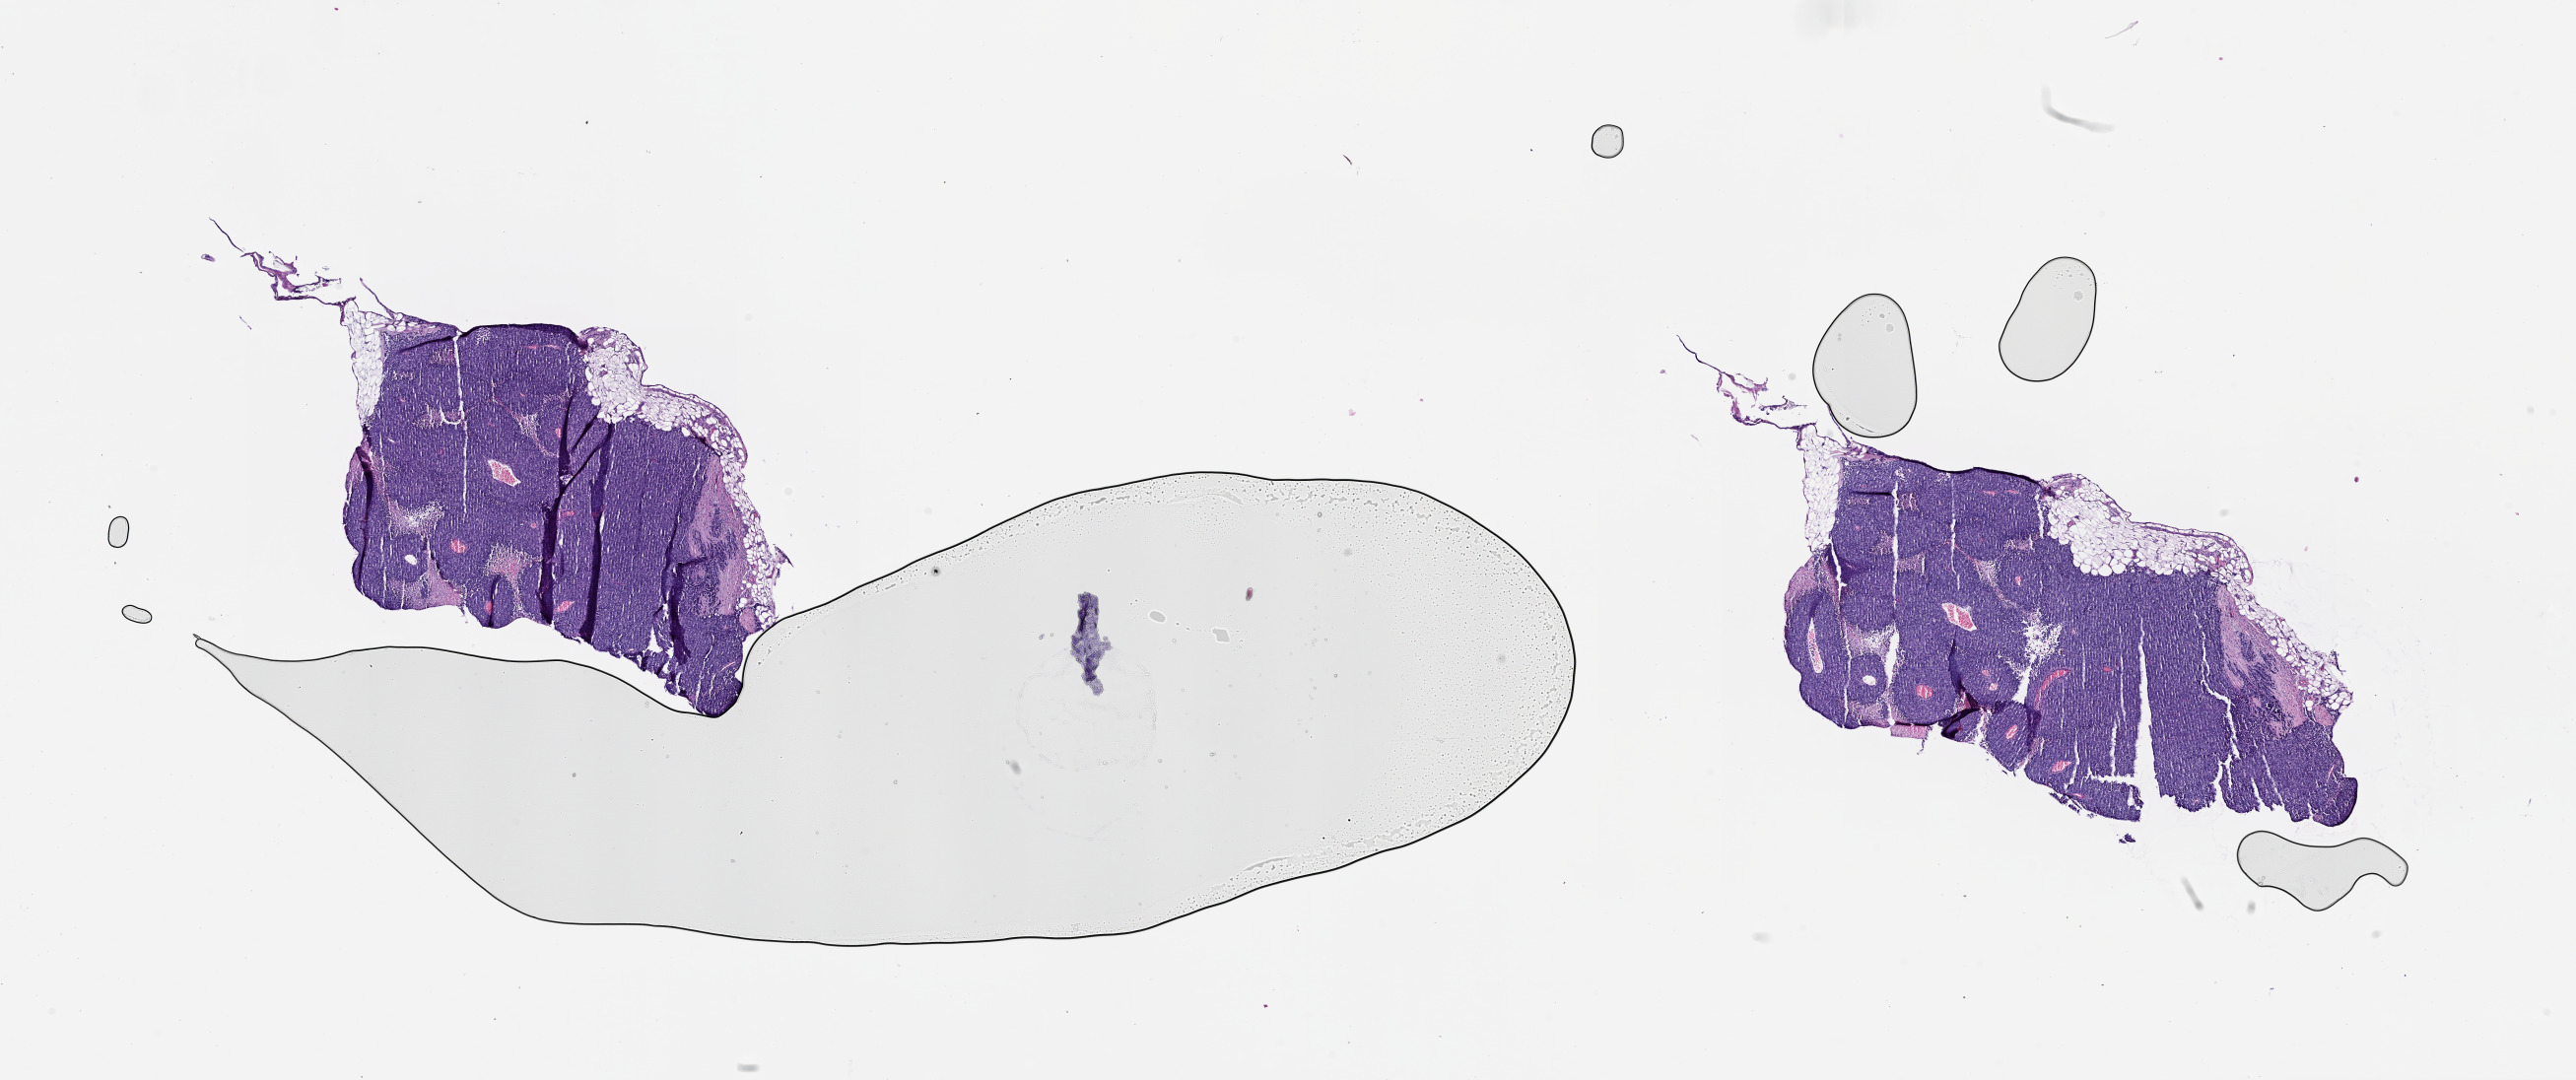
H&E whole-slide image — low-resolution overview of the scanned area, about 21.0 x 8.8 mm (acquisition: 20x scan). 53-year-old male patient.
• patient diagnosis: Malignant melanoma, NOS